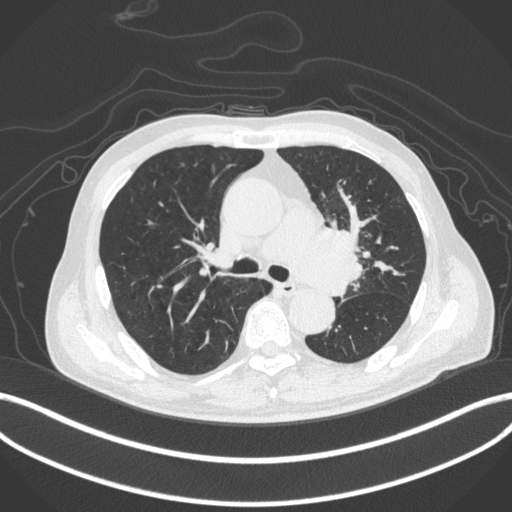
Chest CT, one axial slice; position 276 of 420 along the scan axis; lung window (W 1500 / L -600 HU); 1 mm slice thickness; 512 × 512 image matrix, field of view 400 × 400 mm. Male patient, age 77 years. Case-level facts recorded for this patient, not image findings: clinical TNM (as recorded): T3 N1 M0.
Annotated regions visible in this slice (bounding box drawn by a radiologist):
- lung tumour (recorded histology: adenocarcinoma): bounding box <297,220,363,297> (left, top, right, bottom; pixels)